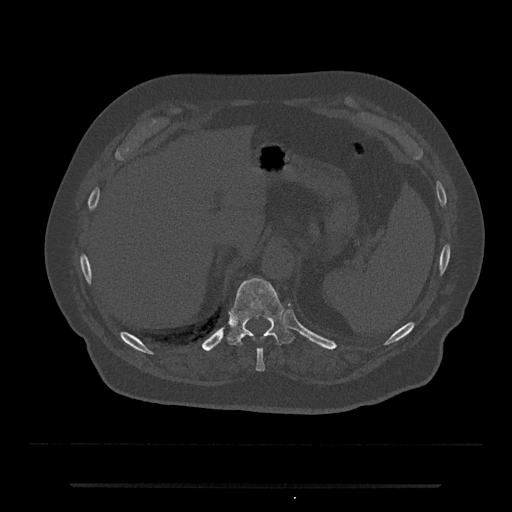
CT including the spine, one axial slice; position 665 of 797 along the scan axis; 120 kVp; bone window (W 1800 / L 400 HU); 0.5 mm slice thickness; 512 × 512 image matrix, field of view 434 × 434 mm. Patient: male, 80 years. From the clinical record (not read from this slice): primary cancer: prostate; vertebrae with lytic lesions (as recorded): L1, T11.
Annotated regions visible in this slice (semi-automatically segmented with operator editing):
- T10 vertebra: bounding box [x1, y1, x2, y2] px = [256, 349, 265, 371]
- T11 vertebra: [226, 278, 295, 346]